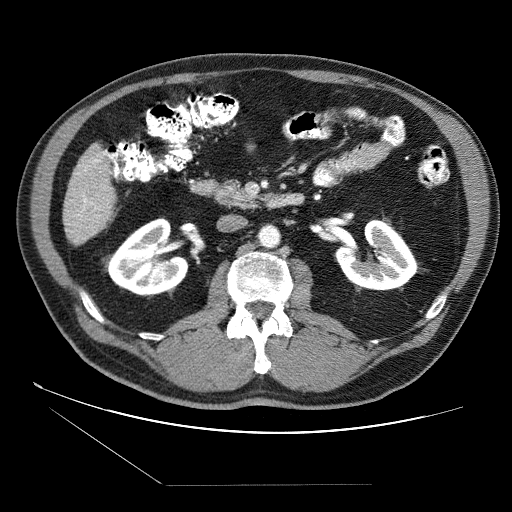
Contrast-enhanced abdominal CT (liver protocol), one axial slice; slice 13 of 87 in the series (ordered by position); reconstruction kernel STANDARD; soft-tissue window (W 400 / L 40 HU); 2.5 mm slice thickness; 512 × 512 image matrix, field of view 400 × 400 mm. From the clinical record (not read from this slice): diagnosis: hepatocellular carcinoma (patient treated with transarterial chemoembolisation; whether this scan precedes or follows treatment is not stated here); TNM stage (as recorded): Stage-II; Child-Pugh class: B; tumour differentiation: no biopsy; tumour size: 2.6 cm.
Annotated regions visible in this slice (semi-automatically segmented with operator editing):
- liver parenchyma outside the tumour (the mass and vessels are separate outlines, so this box may not span the whole liver): bounding box (x1, y1, x2, y2) in pixels: (64, 144, 116, 244)
- liver vessels: (76, 152, 105, 217)